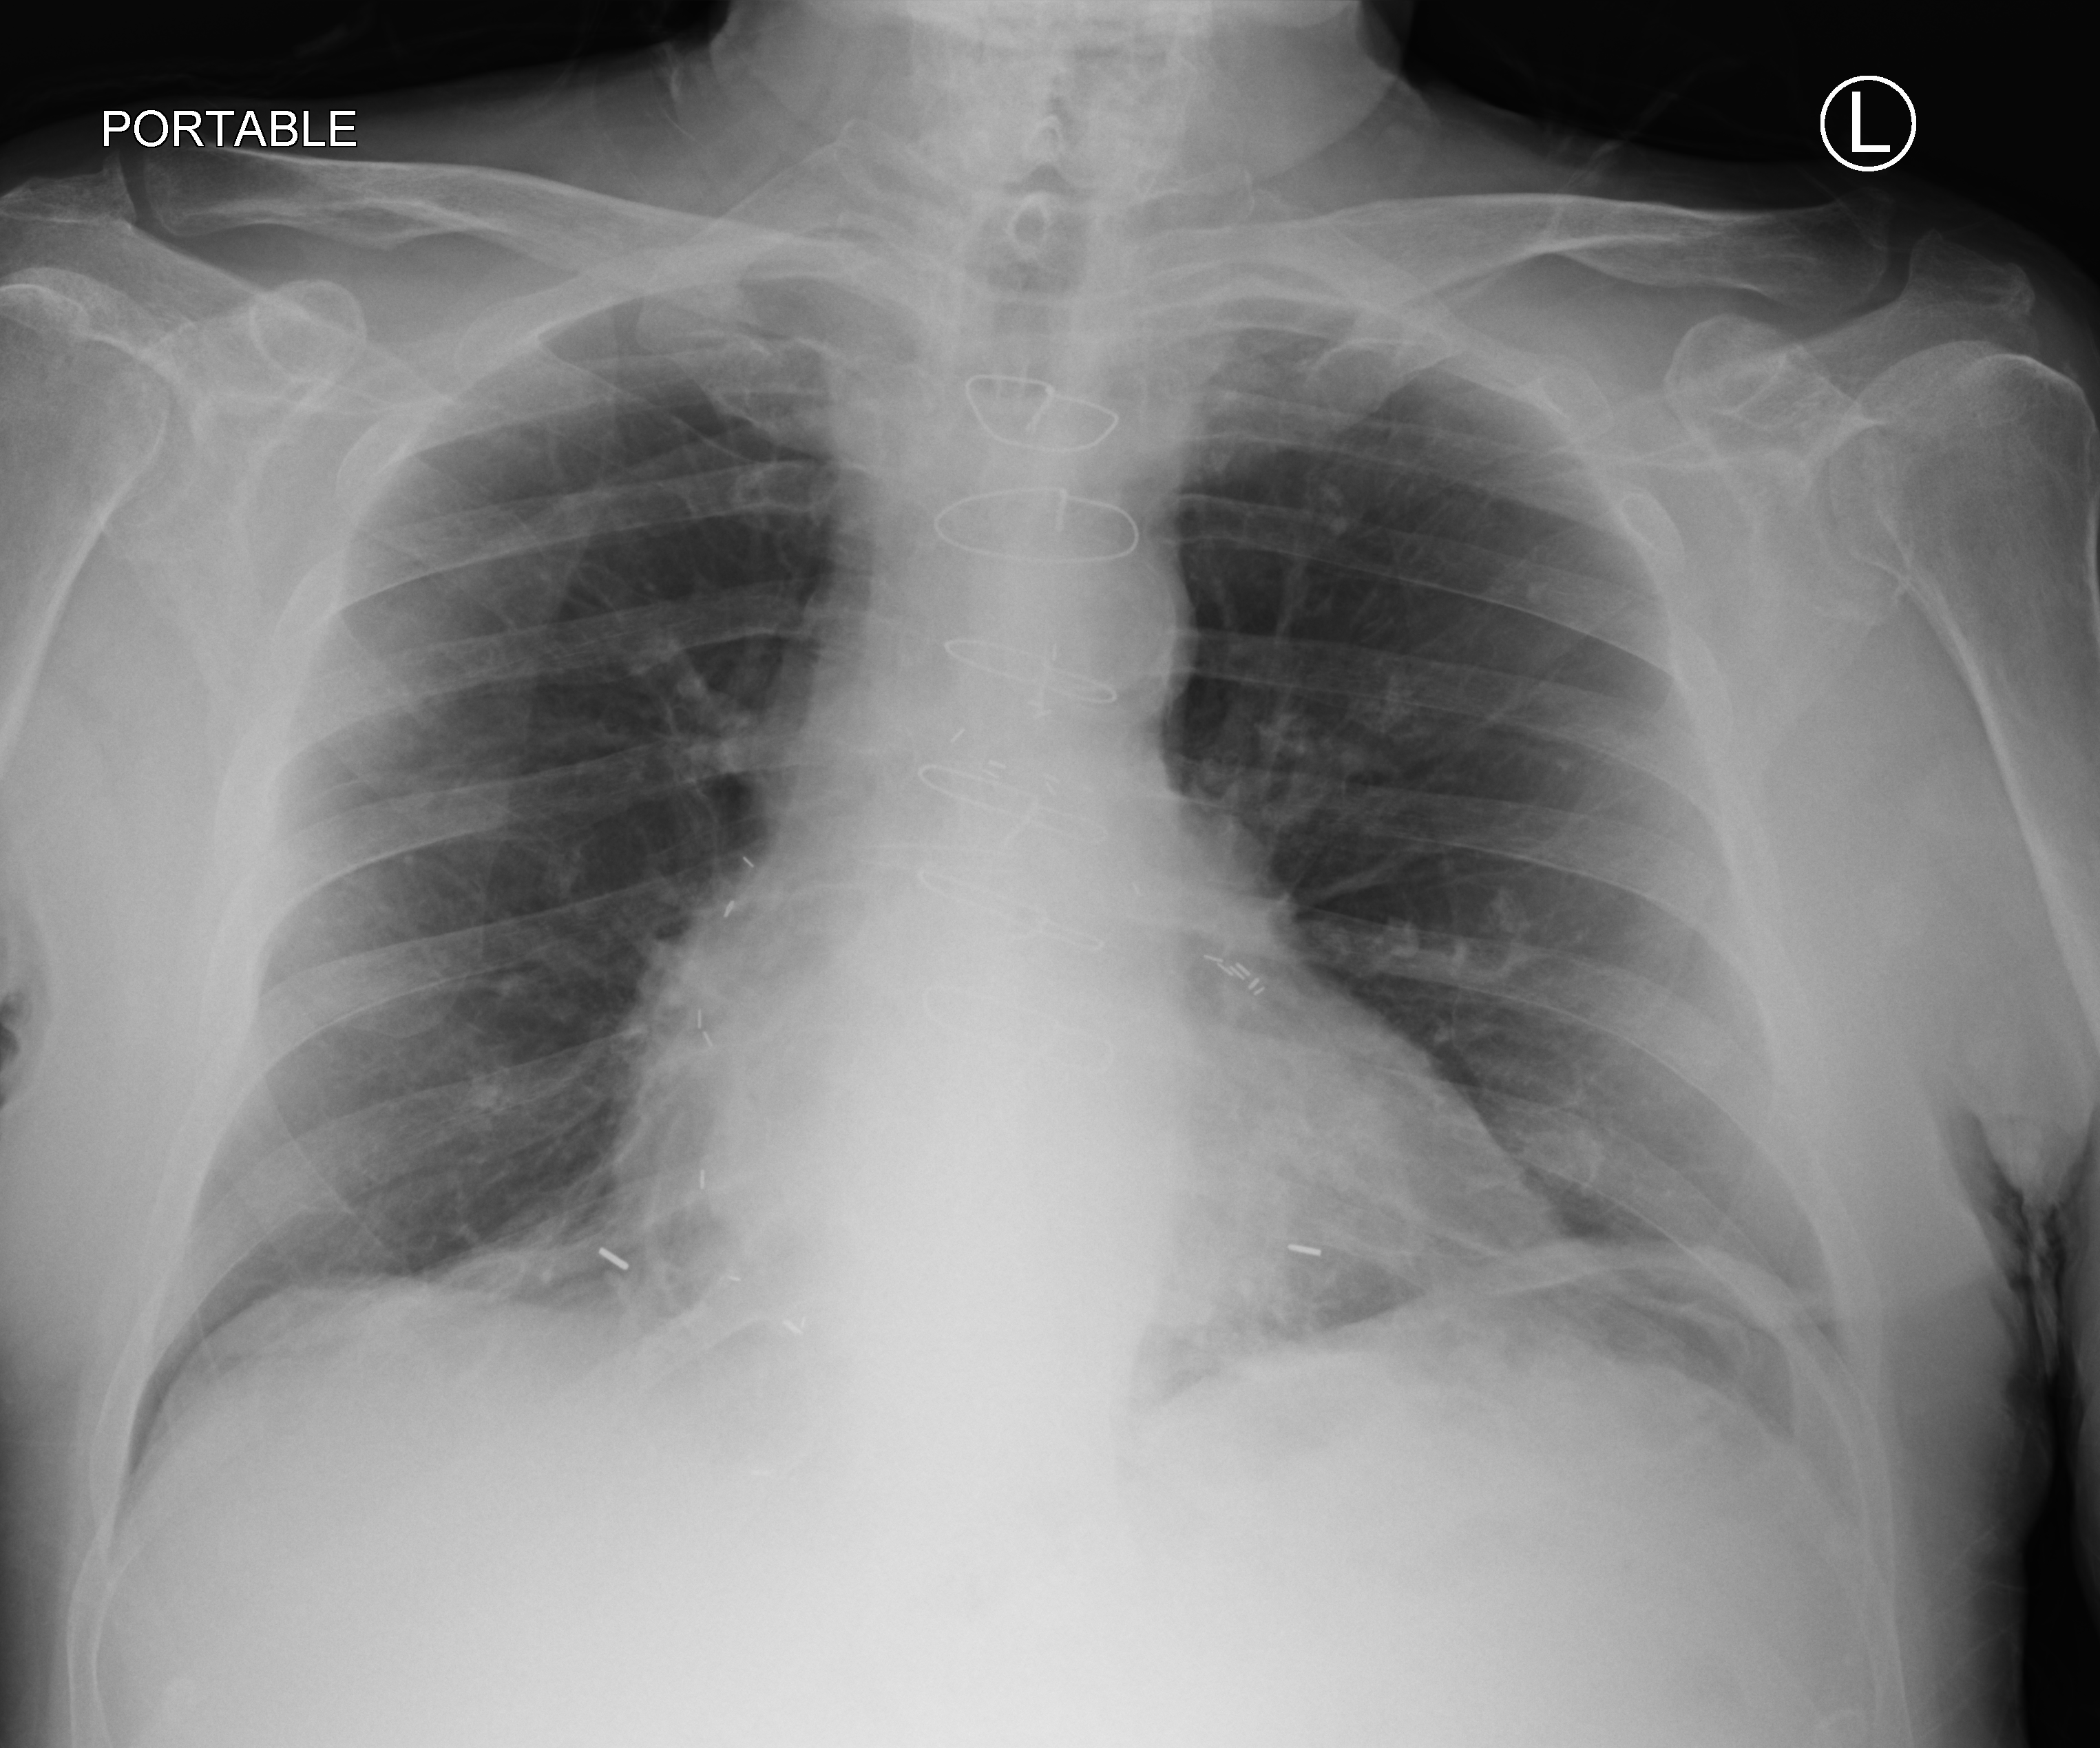
Portable chest radiograph; anteroposterior (AP) projection. Male patient hospitalised with COVID-19, age 75–90 years.
Hospital-stay facts (about this admission, not read from this image; timing relative to this image not recorded):
- admitted to intensive care during this hospital stay: yes
- mechanically ventilated during this hospital stay: yes
- smoking status (admission record): never